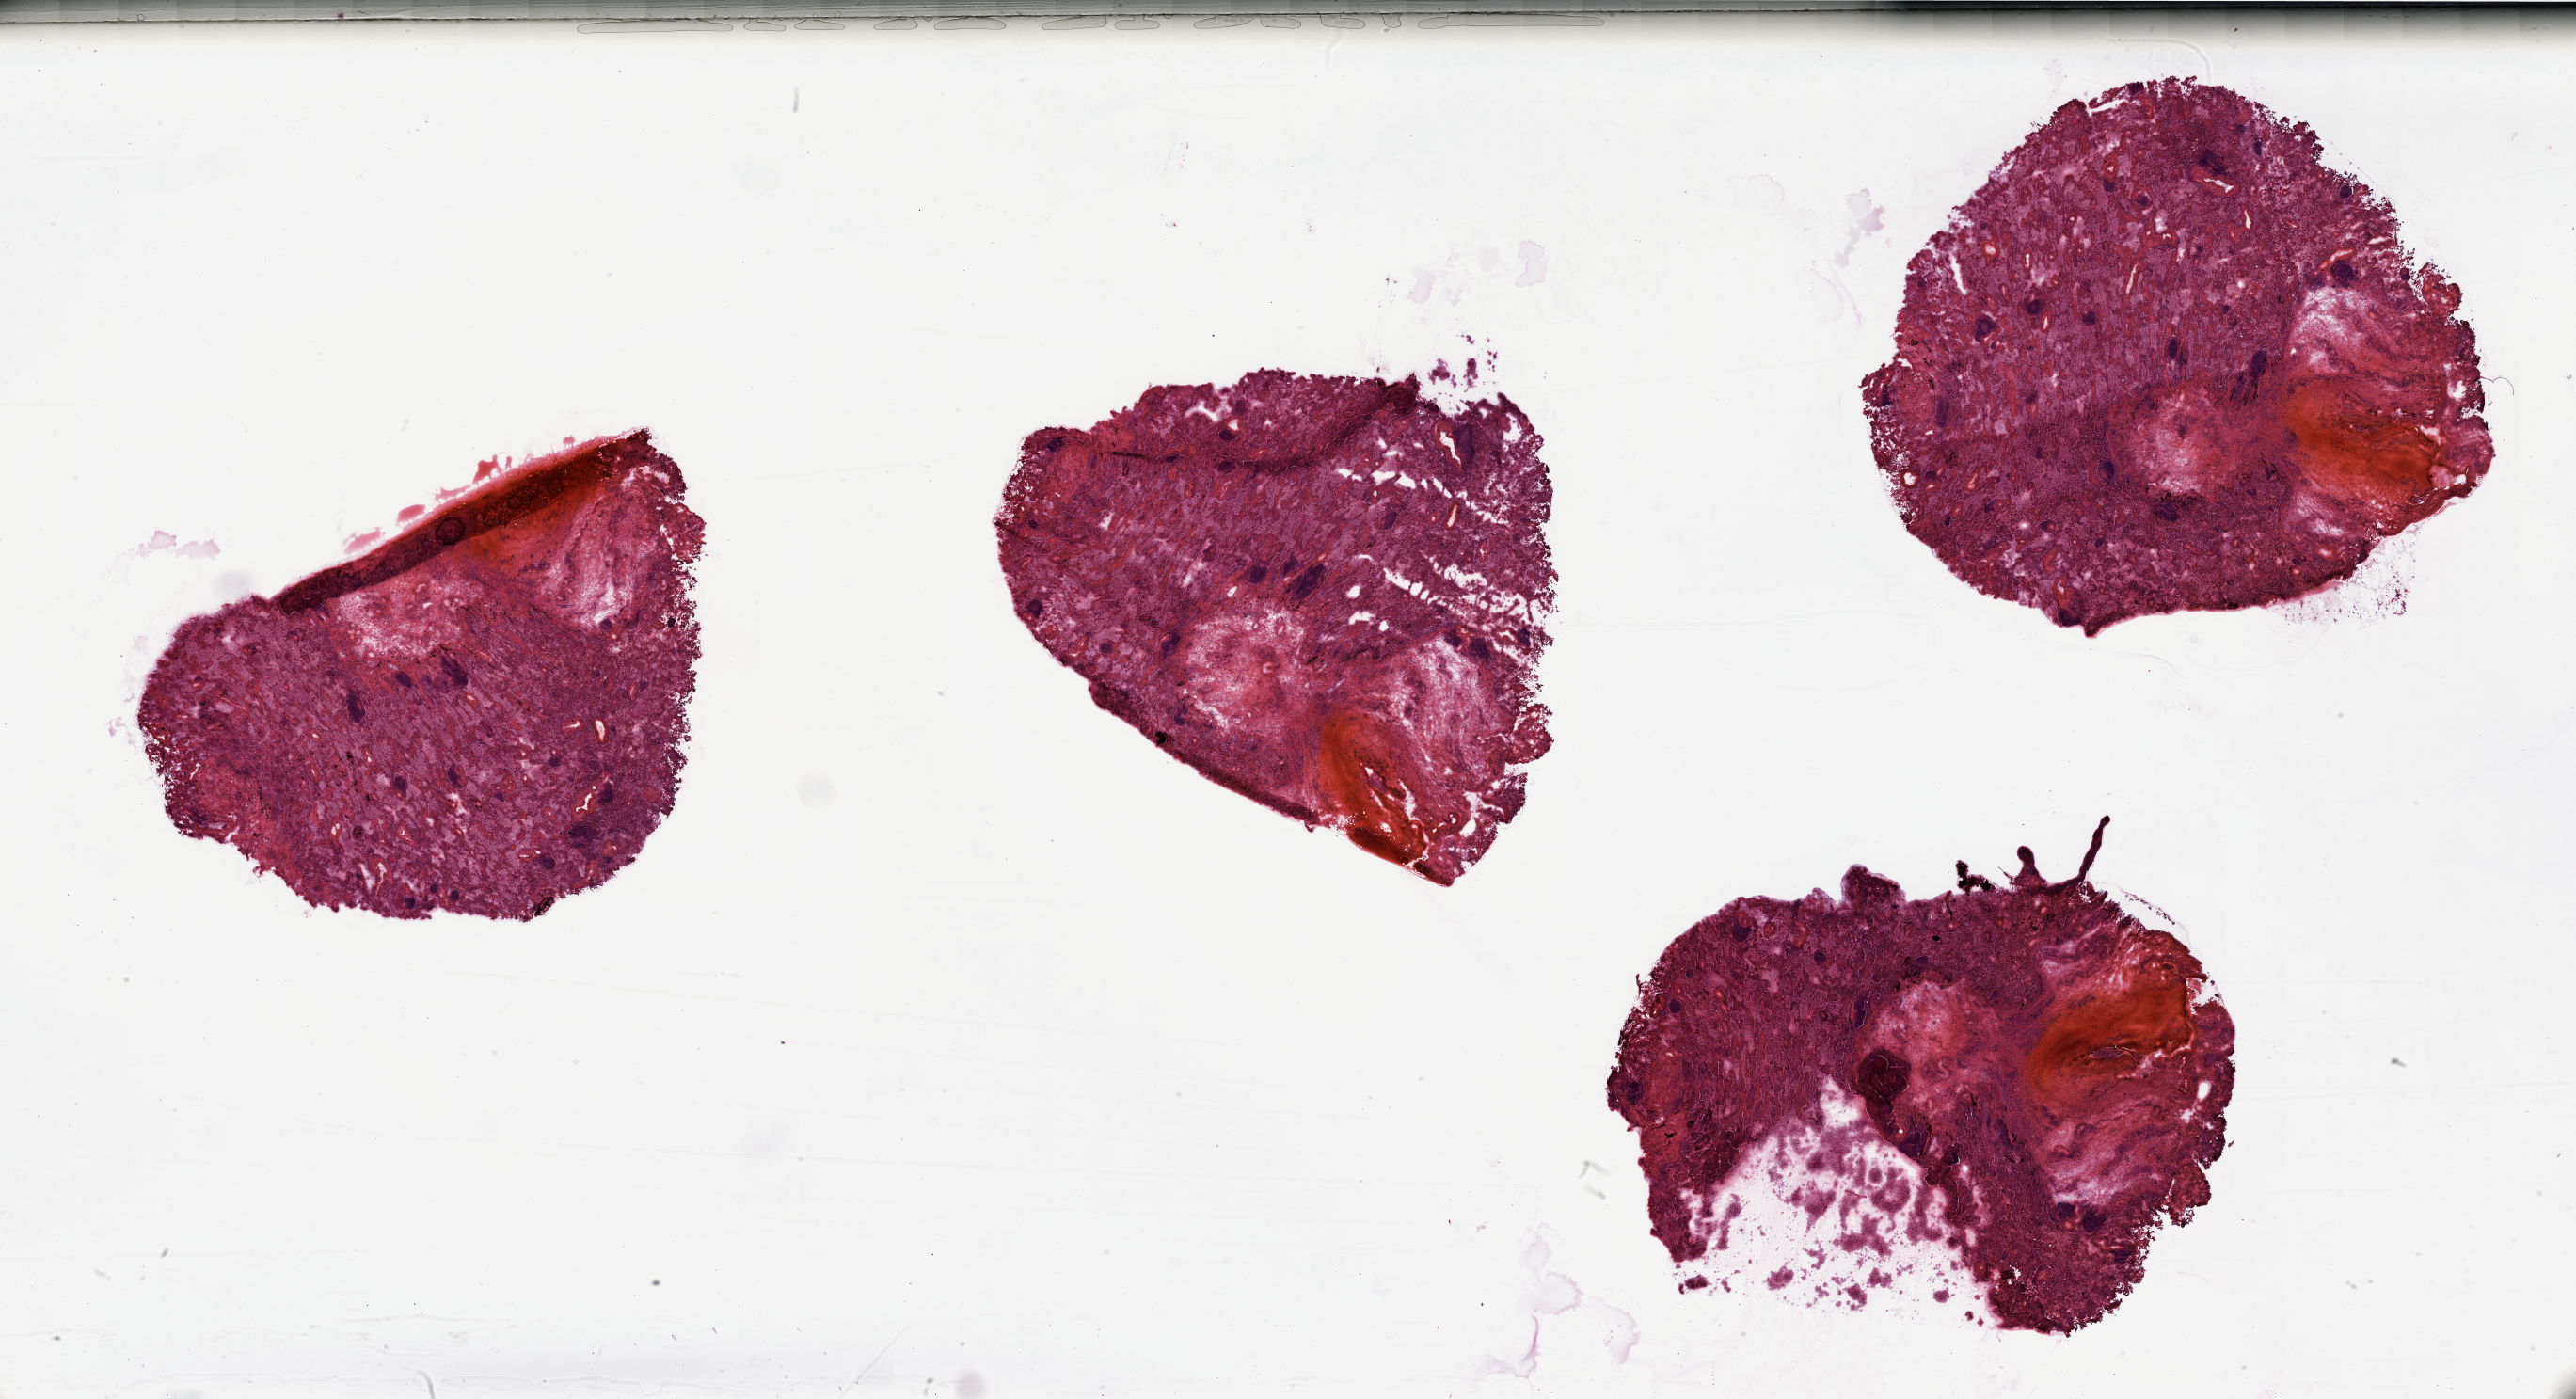
H&E-stained whole-slide image, a low-resolution overview of the entire scanned area, about 43.3 x 23.5 mm (acquisition: 20x scan), tumour tissue sample, lung. 65-year-old male patient.
Primary tumour site (as recorded): left lower lobe. Patient diagnosis (cohort enrolment): squamous cell carcinoma (lung).